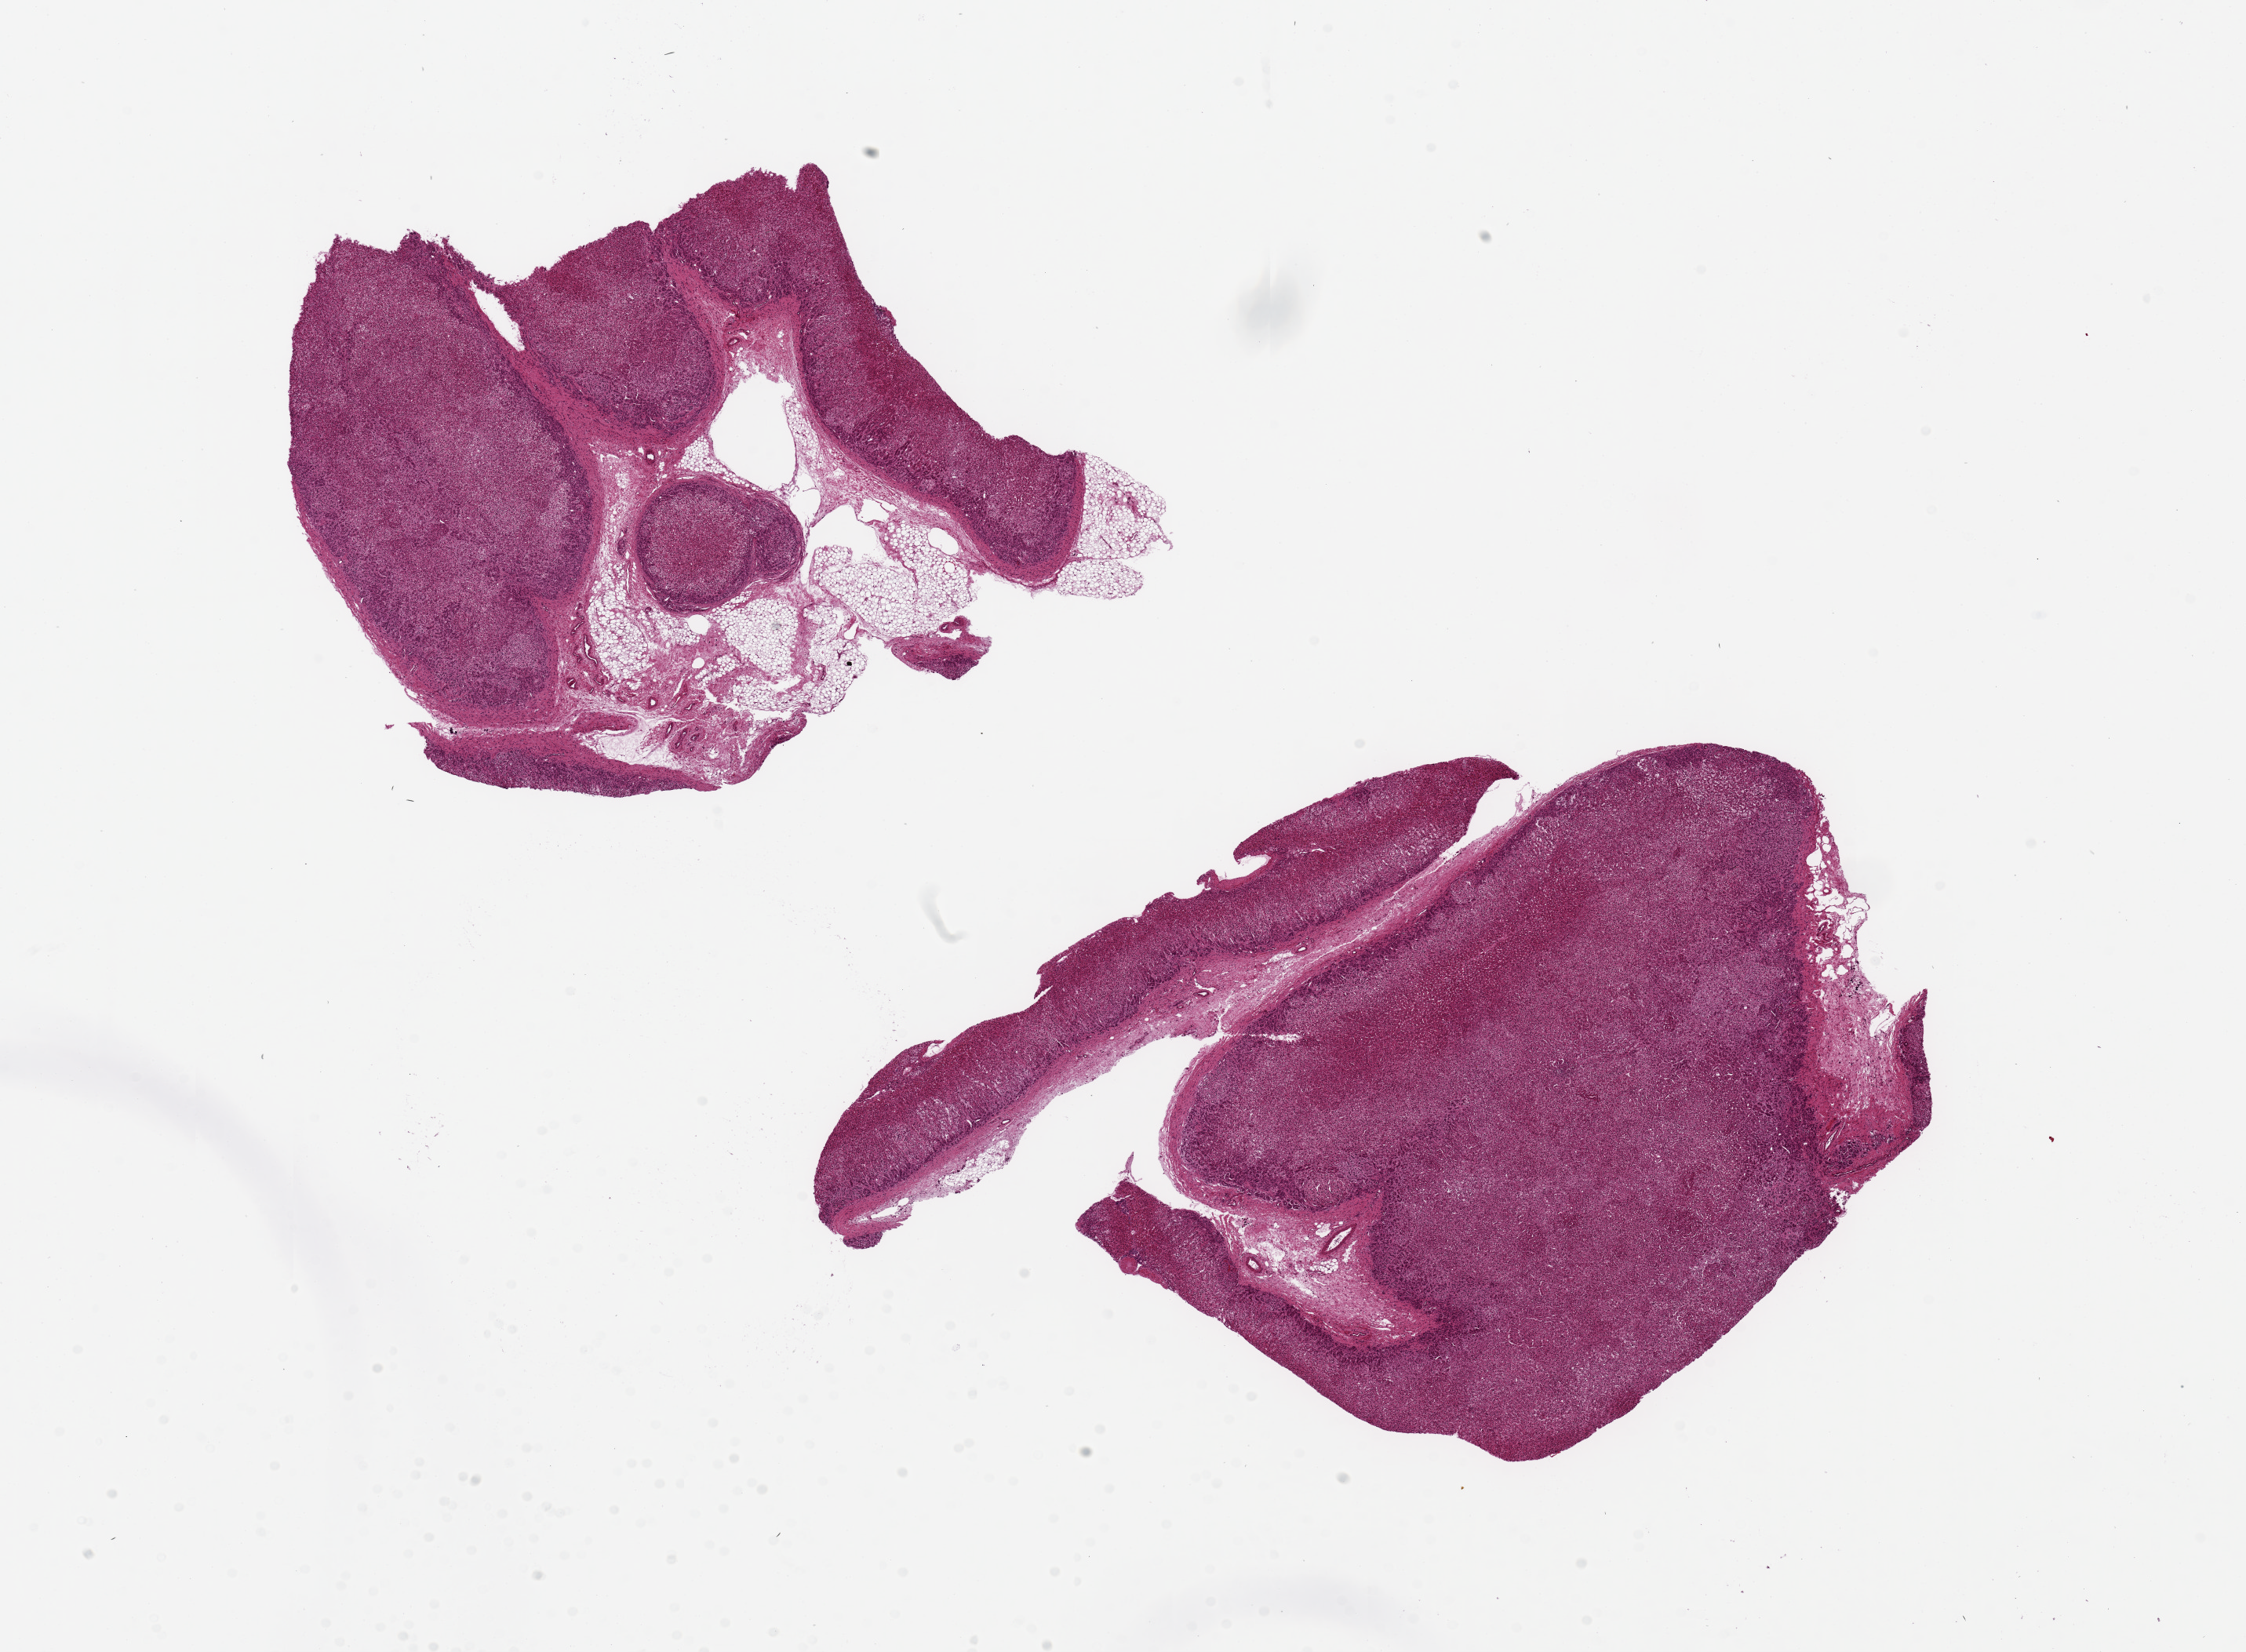
Whole-slide image, H&E stain, brightfield — shown as a low-resolution overview of the whole scanned area (about 22.6 x 16.7 mm, from a 20x scan). PAXgene-fixed, paraffin-embedded tissue. Sampled site (target tissue): adrenal gland. Donor tissue sample. Female donor.
Reviewer comment on this tissue sample: 2 pieces, 8x7 & 10x8mm; cortex; 1 with 30% peripherall adipose; larger piece without adipose.